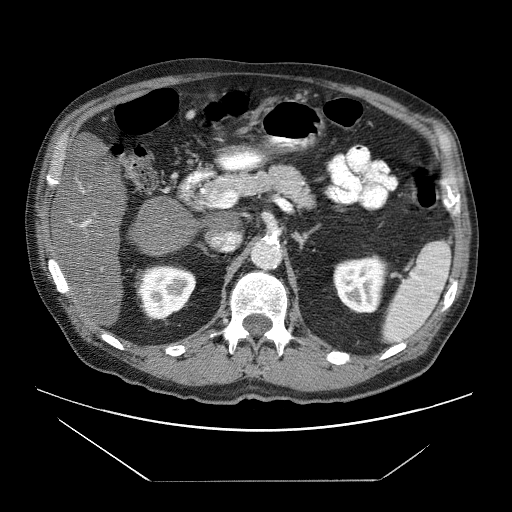
Contrast-enhanced abdominal CT (liver protocol), one axial slice; 120 kVp; soft-tissue window (W 400 / L 40 HU); 2.5 mm slice thickness; 512 × 512 image matrix, field of view 420 × 420 mm. Case-level facts recorded for this patient, not image findings: diagnosis: hepatocellular carcinoma (patient treated with transarterial chemoembolisation; whether this scan precedes or follows treatment is not stated here); TNM stage (as recorded): Stage-IVB; Child-Pugh class: B; tumour differentiation: poorly differentiated.
Annotated regions visible in this slice (semi-automatic segmentation, software-assisted and operator-edited):
- liver parenchyma outside the tumour (the mass and vessels are separate outlines, so this box may not span the whole liver): box from (x=54, y=177) to (x=126, y=327) px
- liver vessels: (x=71, y=190)–(x=91, y=227)